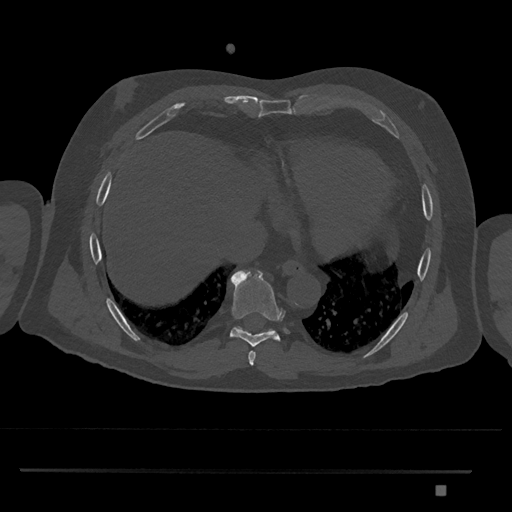
CT including the spine, one axial slice; slice 1103 of 1134 in the series (ordered by position); reconstruction kernel Br40s/3; 120 kVp; bone window (W 1800 / L 400 HU); 512 × 512 image matrix. Male patient, age 65 years. Case-level facts recorded for this patient, not image findings: primary cancer: prostate.
Structures marked on this image (semi-automatic segmentation, software-assisted and operator-edited):
- T8 vertebra: bounding box <230,270,283,347> (left, top, right, bottom; pixels)
- T9 vertebra: <236,326,273,332>